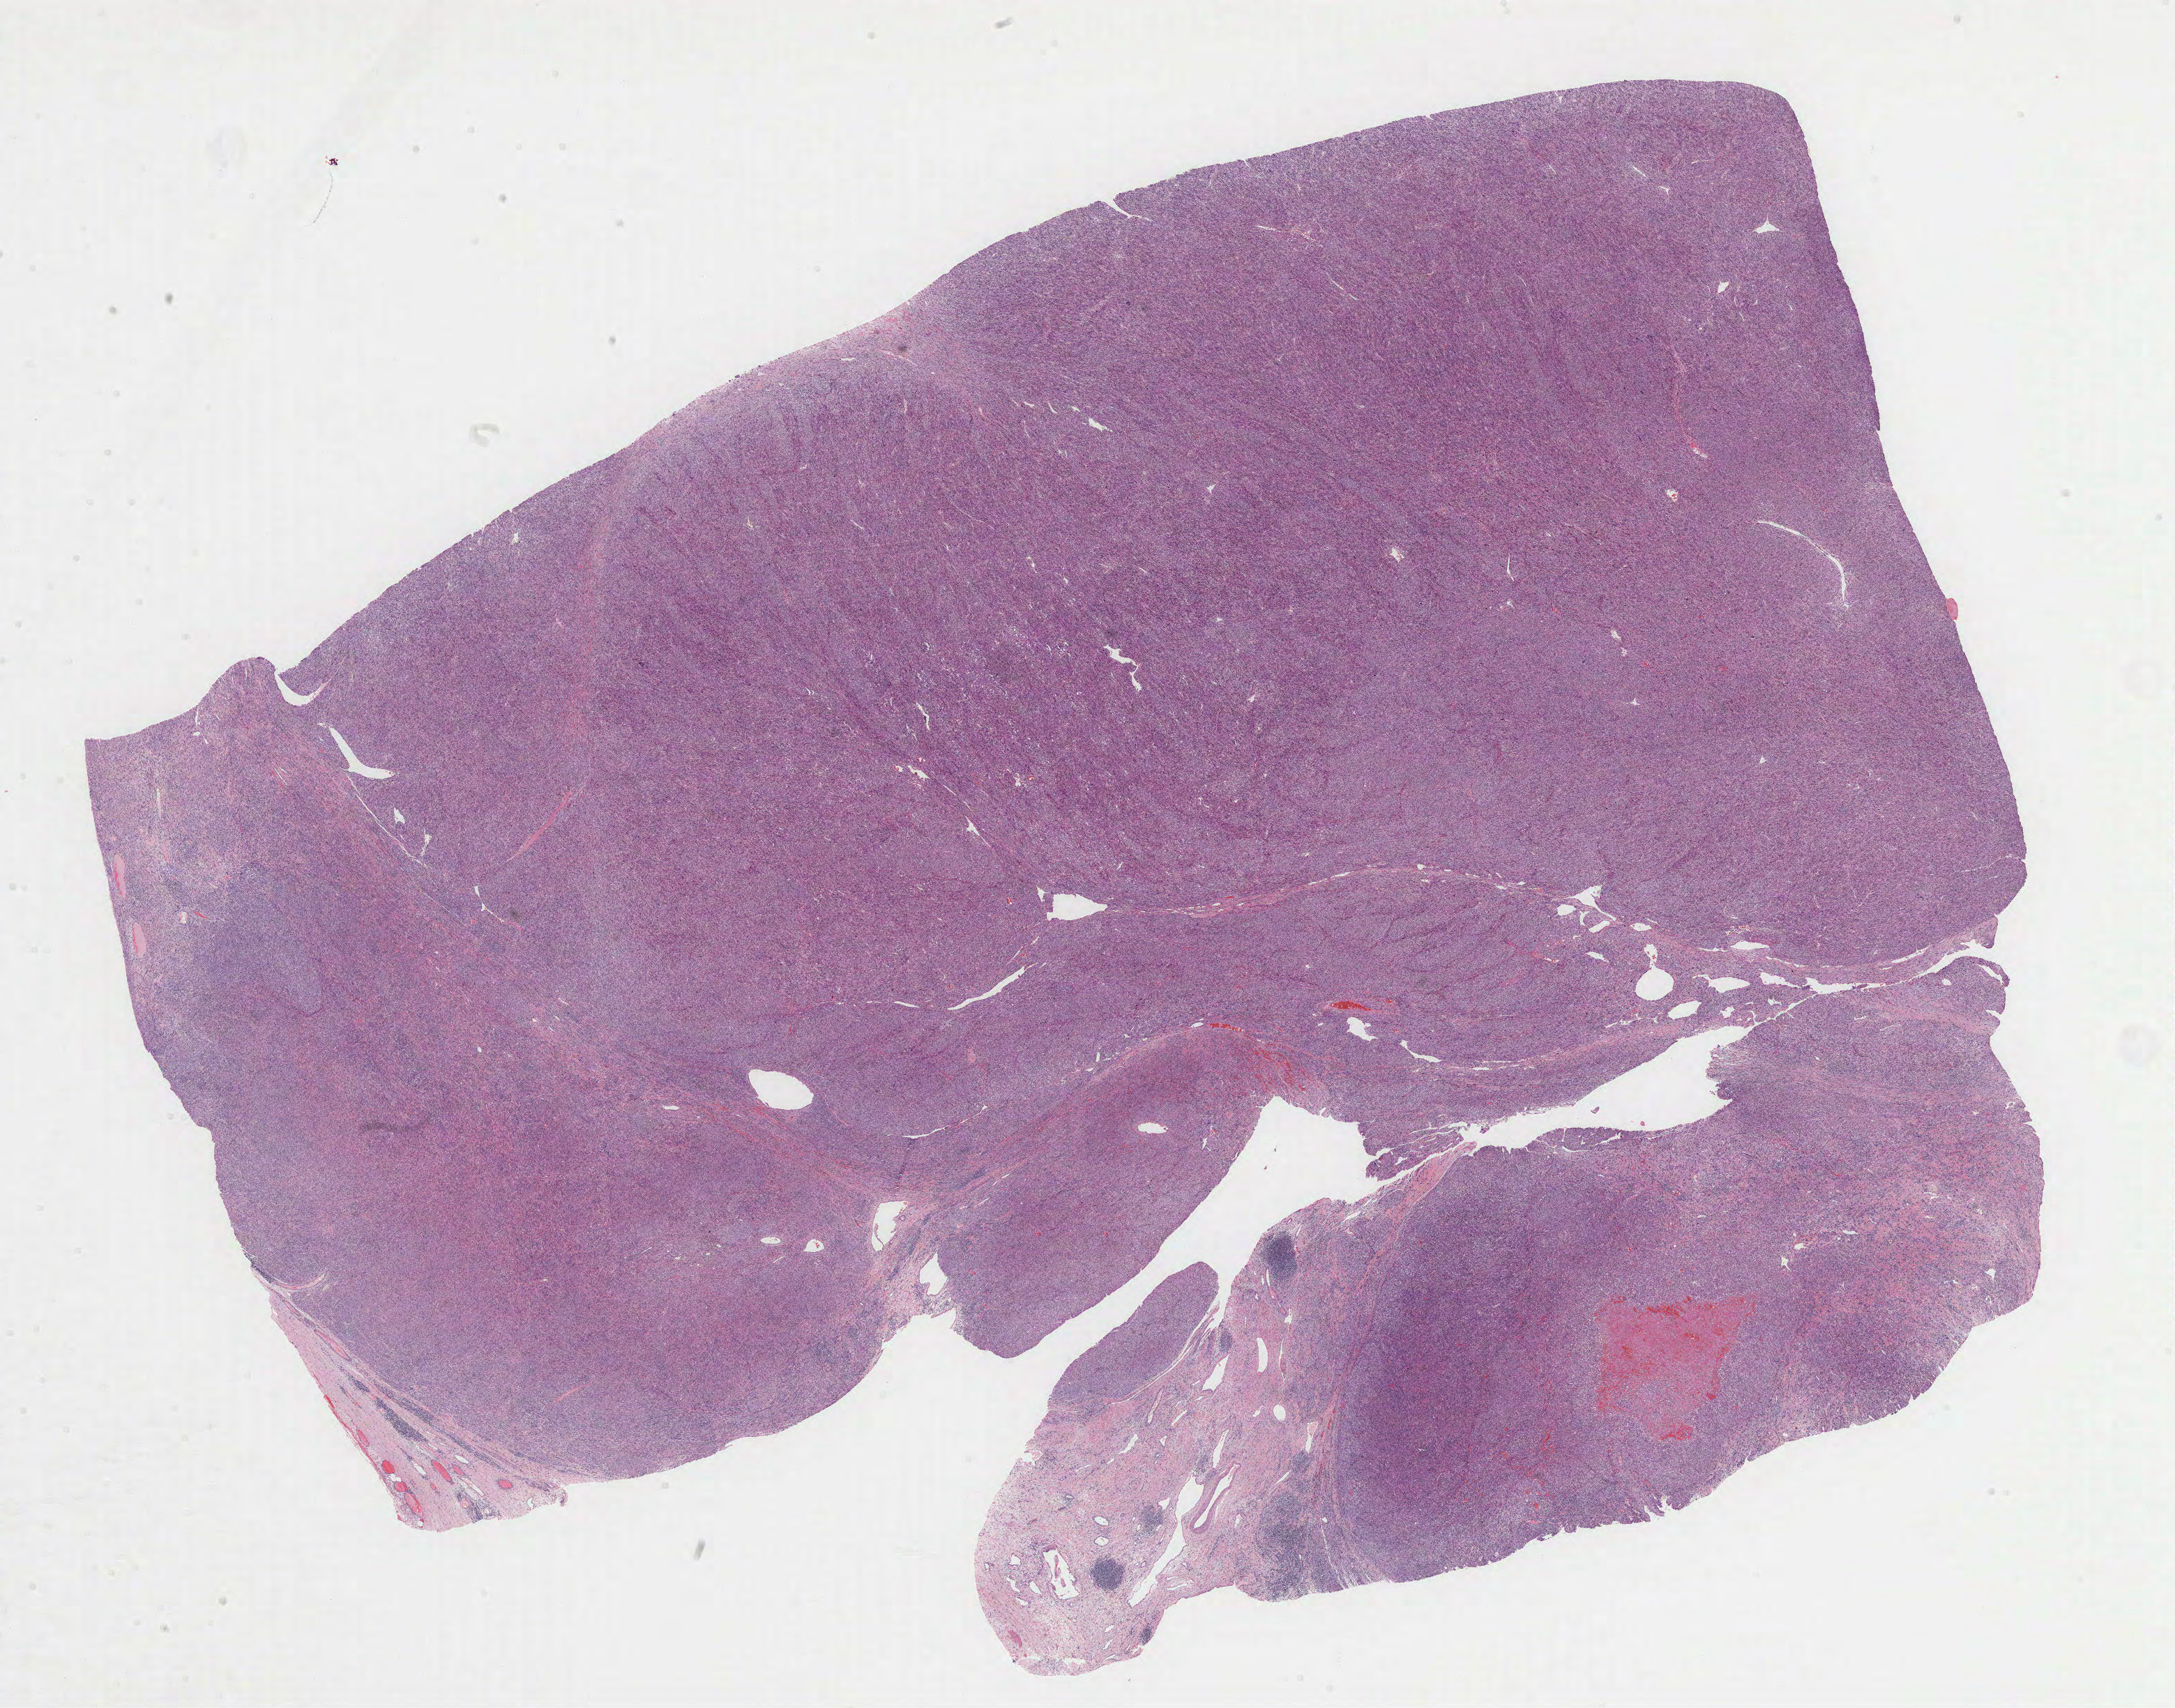
Digitized H&E-stained tissue section (whole slide), shown as a low-resolution overview of the whole scanned area (about 25.2 x 19.8 mm, slide scanned at 40x); formalin-fixed paraffin-embedded (FFPE) diagnostic section; retroperitoneum and peritoneum, primary tumour sample. Patient: female, age at initial diagnosis 53 years.
Diagnosis: Leiomyosarcoma, NOS.